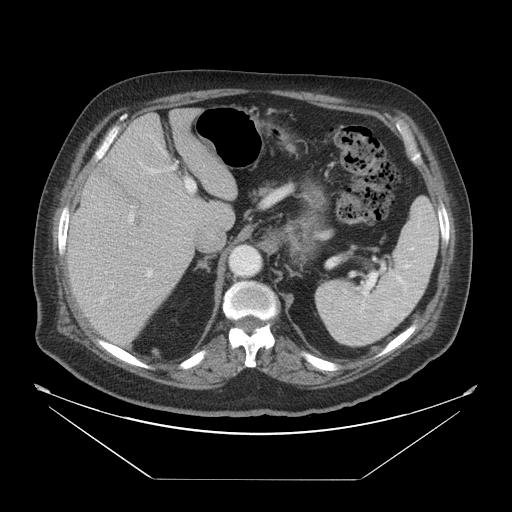
Contrast-enhanced abdominal CT, one axial slice; position 34 of 45 along the scan axis; reconstruction kernel STANDARD; soft-tissue window (W 400 / L 40 HU); 5 mm slice thickness; 512 × 512 image matrix, field of view 463 × 463 mm. Male patient, age 87 years. From the clinical record (not read from this slice): diagnosis: colorectal cancer liver metastases, imaged before liver resection; multiple liver metastases: no; largest metastasis: 4.5 cm; disease in both lobes: yes.
Annotated regions visible in this slice (expert manual segmentation):
- liver: bounding box <67,108,238,349> (left, top, right, bottom; pixels)
- planned liver remnant (the part of the liver to remain after resection): <116,108,238,197>
- portal vein (with intrahepatic branches): <118,162,196,289>
- liver metastasis: <132,209,145,236>
- liver metastasis: <93,158,140,200>